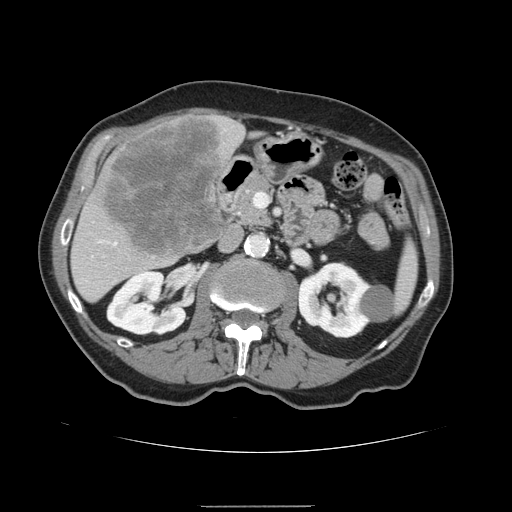
Contrast-enhanced abdominal CT, one axial slice. Position 66 of 168 along the scan axis. Intravenous contrast given. Soft-tissue window (W 400 / L 40 HU). 2.5 mm slice thickness. 512 × 512 image matrix, field of view 386 × 386 mm. Male patient, age 74 years. From the clinical record (not read from this slice): diagnosis: colorectal cancer liver metastases, imaged before liver resection.
Annotated regions visible in this slice (outlined manually by an expert reader):
- liver: bounding box (x1, y1, x2, y2) in pixels: (70, 114, 247, 303)
- planned liver remnant (the part of the liver to remain after resection): (76, 280, 110, 303)
- liver metastasis: (104, 117, 229, 258)